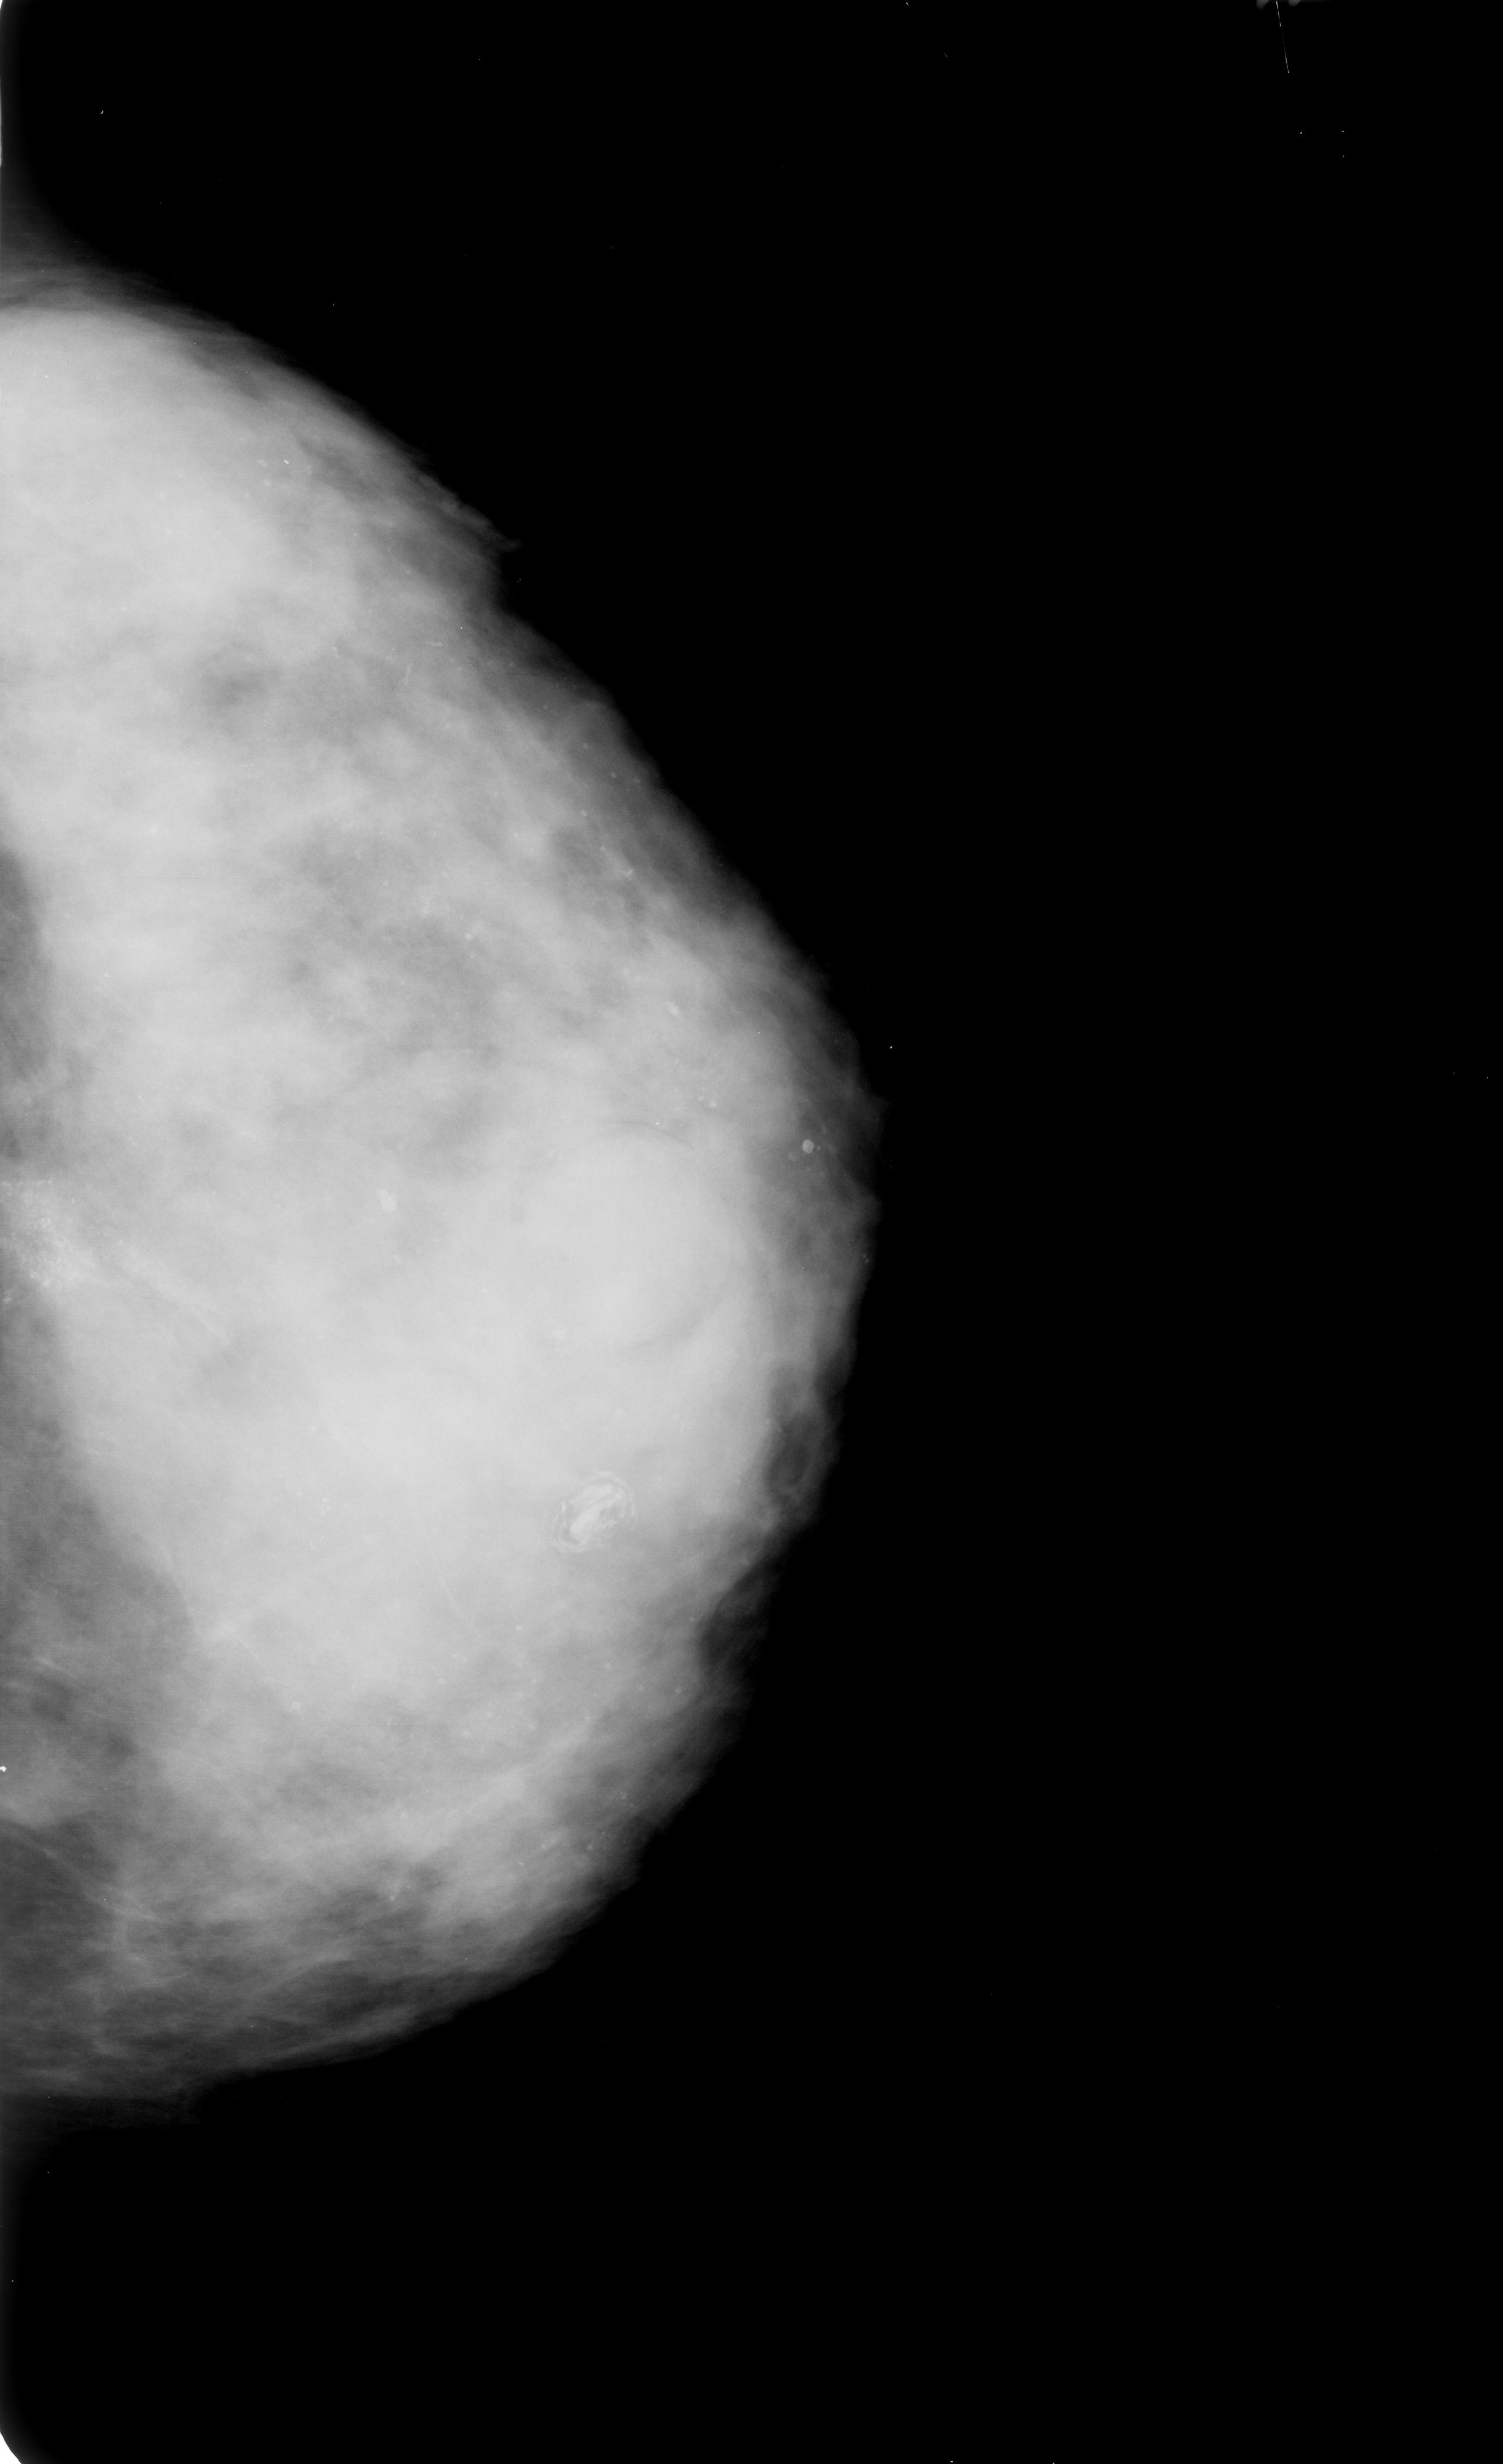
Digitized screen-film mammogram. Left breast. CC view. Breast composition: extremely dense (BI-RADS density category 4 of 4). 1503 × 2464 image matrix.
Marked abnormalities (boxes around the expert regions of interest):
- calcifications, morphology pleomorphic, distribution clustered; BI-RADS assessment category 4; subtlety rating 3 on a 1 (subtle) to 5 (obvious) scale; pathology (as recorded): malignant: bounding box <0,1128,165,1362> (left, top, right, bottom; pixels)